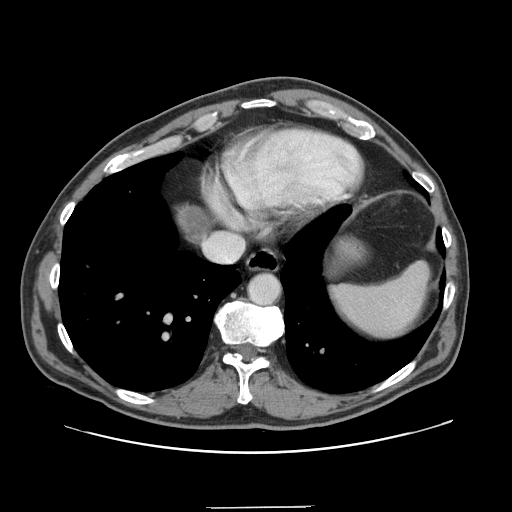
Contrast-enhanced abdominal CT, one axial slice. Position 133 of 139 along the scan axis. 120 kVp. Intravenous contrast given. Soft-tissue window (W 400 / L 40 HU). 2.5 mm slice thickness. 512 × 512 image matrix, field of view 397 × 397 mm. Male patient, age 64 years. From the clinical record (not read from this slice): diagnosis: colorectal cancer liver metastases, imaged before liver resection; multiple liver metastases: yes.
Outlined on this slice (expert manual segmentation):
- liver: bounding box [x1, y1, x2, y2] px = [179, 208, 210, 240]
- liver metastasis: [185, 212, 208, 239]